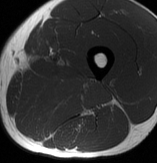
MRI of an extremity soft-tissue mass, one axial slice; slice 33 of 70 in the series (ordered by position); MR volume resampled by the dataset authors to the PET/CT grid (not the native acquisition matrix); 3.27 mm slice thickness; 157 × 163 image matrix, field of view 153 × 159 mm. Male patient. Case-level facts recorded for this patient, not image findings: histological type: extraskeletal osteosarcoma; grade: high; site of the primary tumour: left adductur.
Annotated regions visible in this slice (expert contour drawn on MRI and transferred to this co-registered scan by the dataset authors):
- gross tumour volume (mass): bounding box <12,69,112,137> (left, top, right, bottom; pixels)